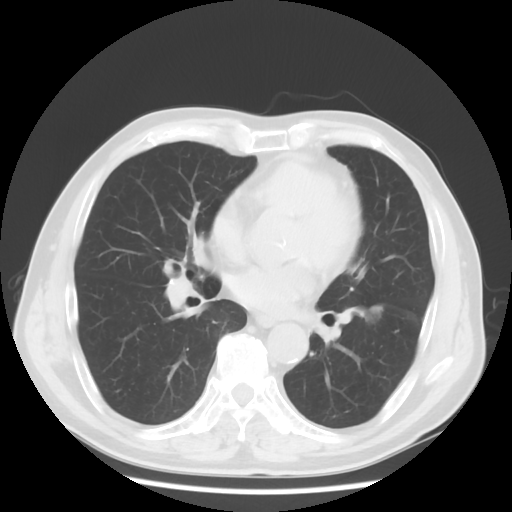
Chest CT, one axial slice. Position 31 of 68 along the scan axis. 120 kVp. Lung window (W 1500 / L -600 HU). 512 × 512 image matrix, field of view 360 × 360 mm. Patient: male, 71 years. From the clinical record (not read from this slice): clinical TNM (as recorded): T1c N1 M0.
Outlined on this slice (rectangle marked by the reading radiologist):
- lung tumour (recorded histology: adenocarcinoma): bounding box (x1, y1, x2, y2) in pixels: (359, 298, 389, 328)